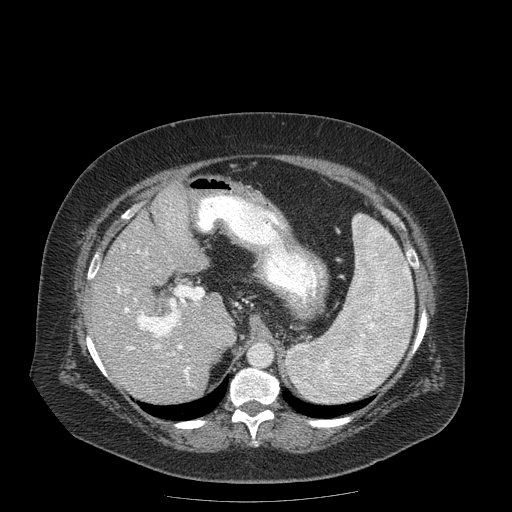
Contrast-enhanced abdominal CT (liver protocol), one axial slice; position 115 of 204 along the scan axis; reconstruction kernel STANDARD; soft-tissue window (W 400 / L 40 HU); 2.5 mm slice thickness; 512 × 512 image matrix, field of view 440 × 440 mm. Case-level facts recorded for this patient, not image findings: diagnosis: hepatocellular carcinoma (patient treated with transarterial chemoembolisation; whether this scan precedes or follows treatment is not stated here); TNM stage (as recorded): Stage-IIIB; Child-Pugh class: A; tumour nodularity: uninodular.
Annotated regions visible in this slice (semi-automatic segmentation, software-assisted and operator-edited):
- liver parenchyma outside the tumour (the mass and vessels are separate outlines, so this box may not span the whole liver): bounding box [x1, y1, x2, y2] px = [90, 182, 234, 402]
- liver vessels: [109, 223, 198, 385]